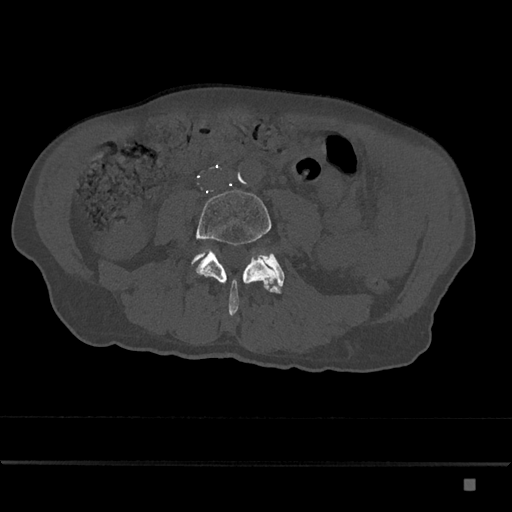
CT including the spine, one axial slice; position 327 of 797 along the scan axis; 120 kVp; bone window (W 1800 / L 400 HU); 512 × 512 image matrix, field of view 390 × 390 mm. Patient: male, 72 years. From the clinical record (not read from this slice): primary cancer: prostate.
Annotated regions visible in this slice (semi-automatic segmentation, software-assisted and operator-edited):
- L4 vertebra: bounding box [x1, y1, x2, y2] px = [193, 190, 283, 316]
- L5 vertebra: [192, 250, 285, 294]